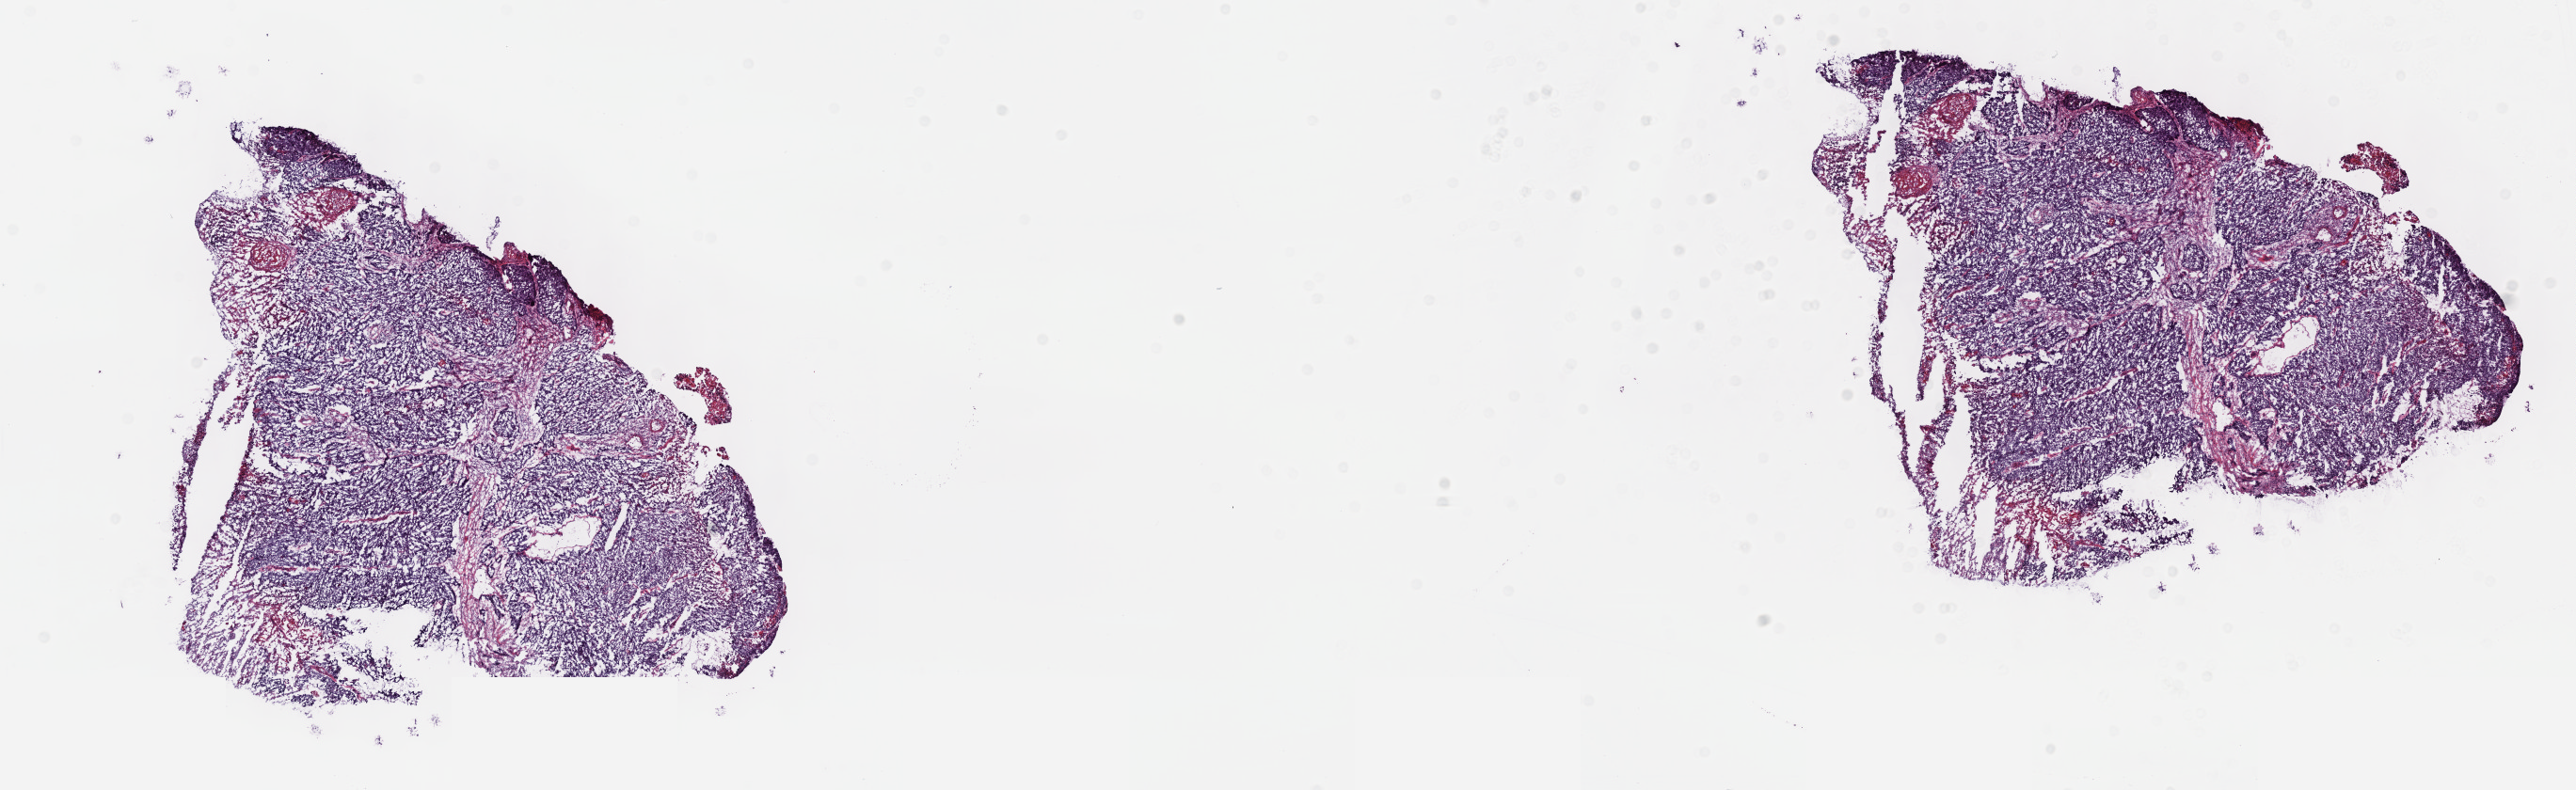
H&E whole-slide image — shown as a low-resolution overview of the whole scanned area (about 22.1 x 6.8 mm), frozen section from the top of the tissue portion, primary tumour sample from the cervix. Female patient; age at initial diagnosis 55 years.
Pathologic diagnosis: Squamous cell carcinoma, NOS.